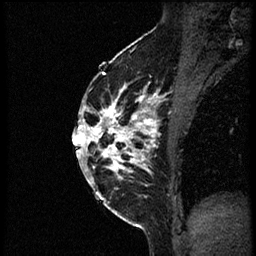
Breast MRI (dynamic contrast-enhanced), one sagittal slice; position 35 of 56 along the scan axis; dynamic contrast-enhanced study with each time point stored as its own series, time point 2 of 3 at this slice position (early post-contrast, ordered by acquisition time); 1.5 T; TE 4.2 ms, TR 21.3 ms; 2 mm slice thickness; 256 × 256 image matrix. Female patient, age 41 years. From the clinical record (not read from this slice): setting: breast cancer imaged before/during neoadjuvant chemotherapy; receptor status: HER2-positive.
Structures marked on this image (semi-automatic segmentation, software-assisted and operator-edited):
- analysis volume of interest (the breast-tissue region the enhancement analysis was run in; not a lesion): bounding box [x1, y1, x2, y2] px = [84, 73, 177, 205]
- tumour enhancement mask (voxels above the 100 % enhancement threshold inside the analysis volume of interest): [84, 73, 163, 184]